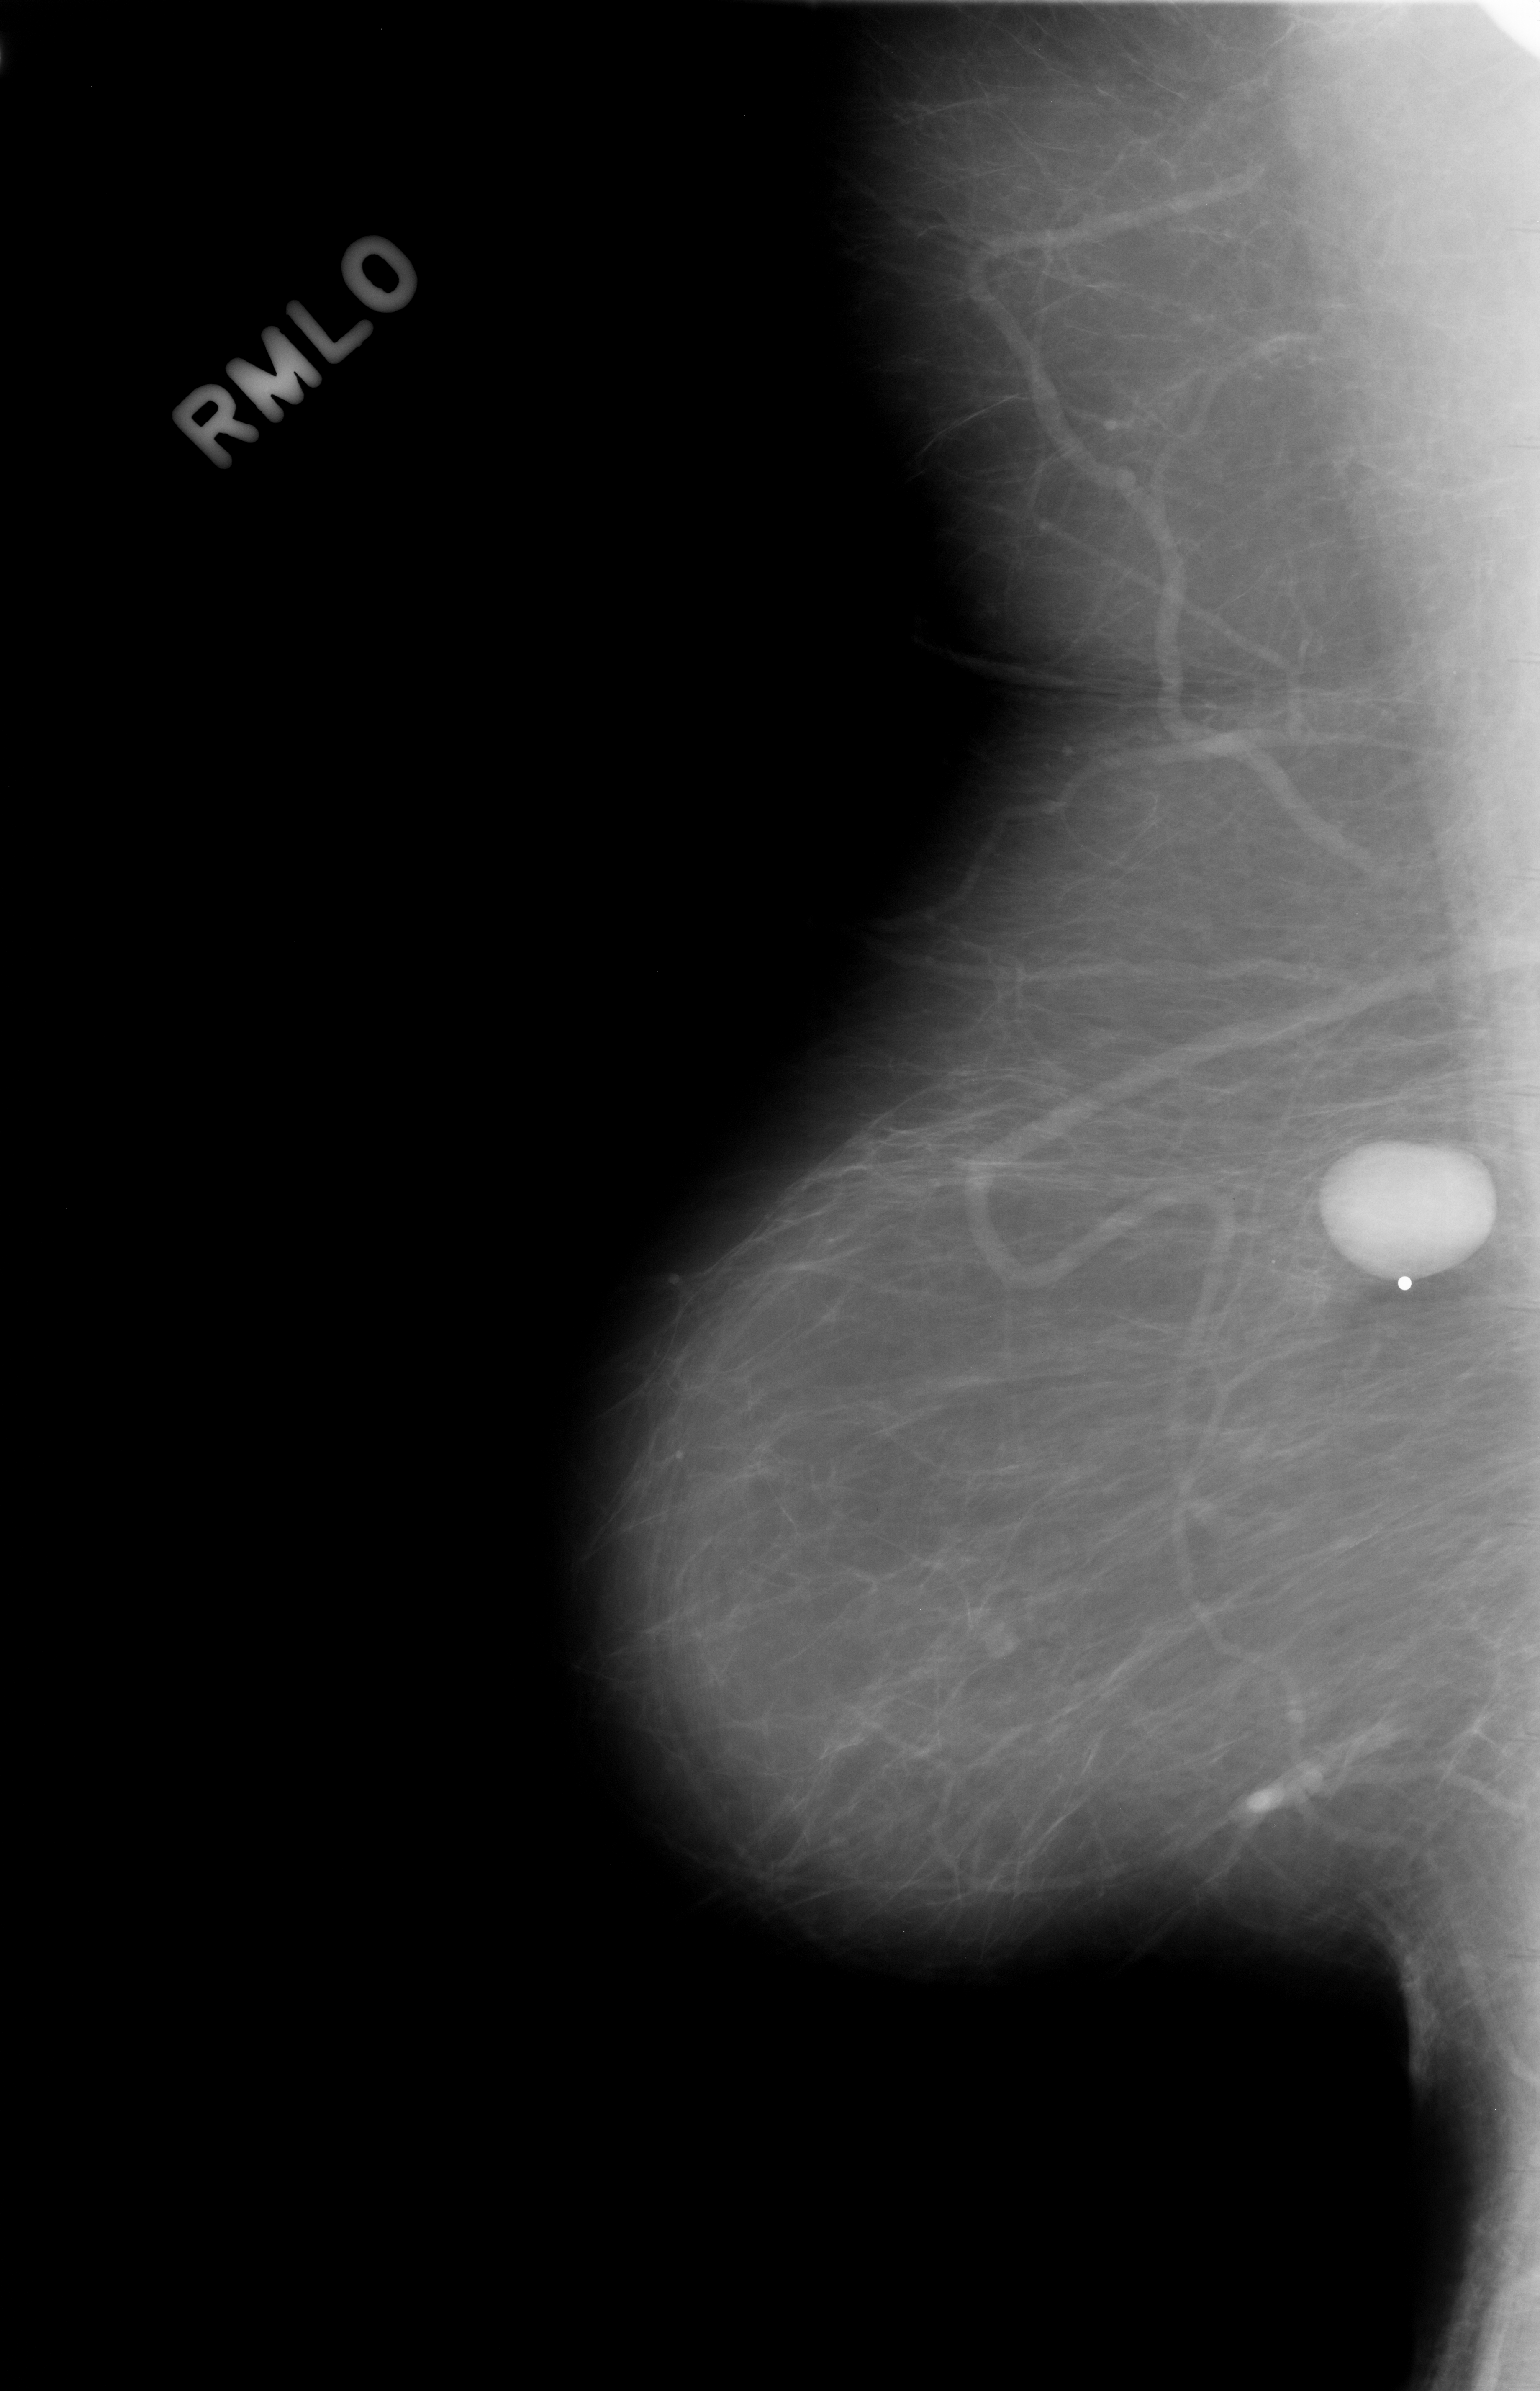
Mammogram (digitized film). Right breast. Mediolateral oblique (MLO) view. BI-RADS breast density category 1 (scale 1–4). 1540 × 2391 image matrix.
Marked abnormalities (boxes around the expert regions of interest):
- mass, shape oval, margins circumscribed; BI-RADS assessment category 4; subtlety rating 5 on a 1 (subtle) to 5 (obvious) scale; pathology result (as recorded, not read from the image): benign: bounding box <1310,1136,1488,1293> (left, top, right, bottom; pixels)